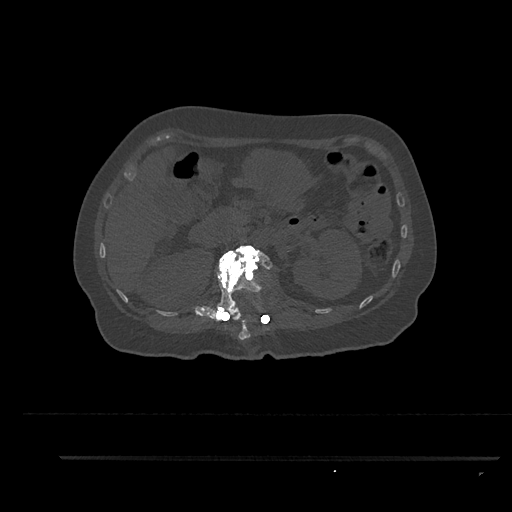
CT including the spine, one axial slice; slice 228 of 797 in the series (ordered by position); reconstruction kernel Br40s/3; 120 kVp; bone window (W 1800 / L 400 HU); 512 × 512 image matrix, field of view 408 × 408 mm. Patient: female, 44 years. Case-level facts recorded for this patient, not image findings: primary cancer: renal.
Annotated regions visible in this slice (semi-automatic segmentation, software-assisted and operator-edited):
- L1 vertebra: bounding box <207,243,273,323> (left, top, right, bottom; pixels)
- T12 vertebra: <229,309,252,340>